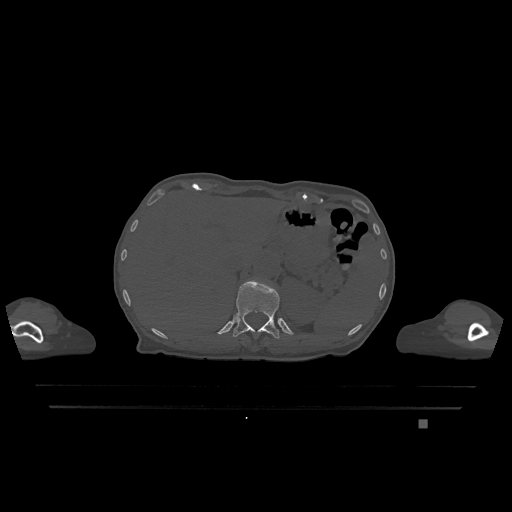
CT including the spine, one axial slice; bone window (W 1800 / L 400 HU); 0.5 mm slice thickness; 512 × 512 image matrix, field of view 500 × 500 mm. Patient: female, 74 years. Case-level facts recorded for this patient, not image findings: primary cancer: lung; vertebrae with lytic lesions (as recorded): T1, T4, T5, T6, L4, L5.
Annotated regions visible in this slice (semi-automatically segmented with operator editing):
- T12 vertebra: box from (x=233, y=280) to (x=280, y=339) px